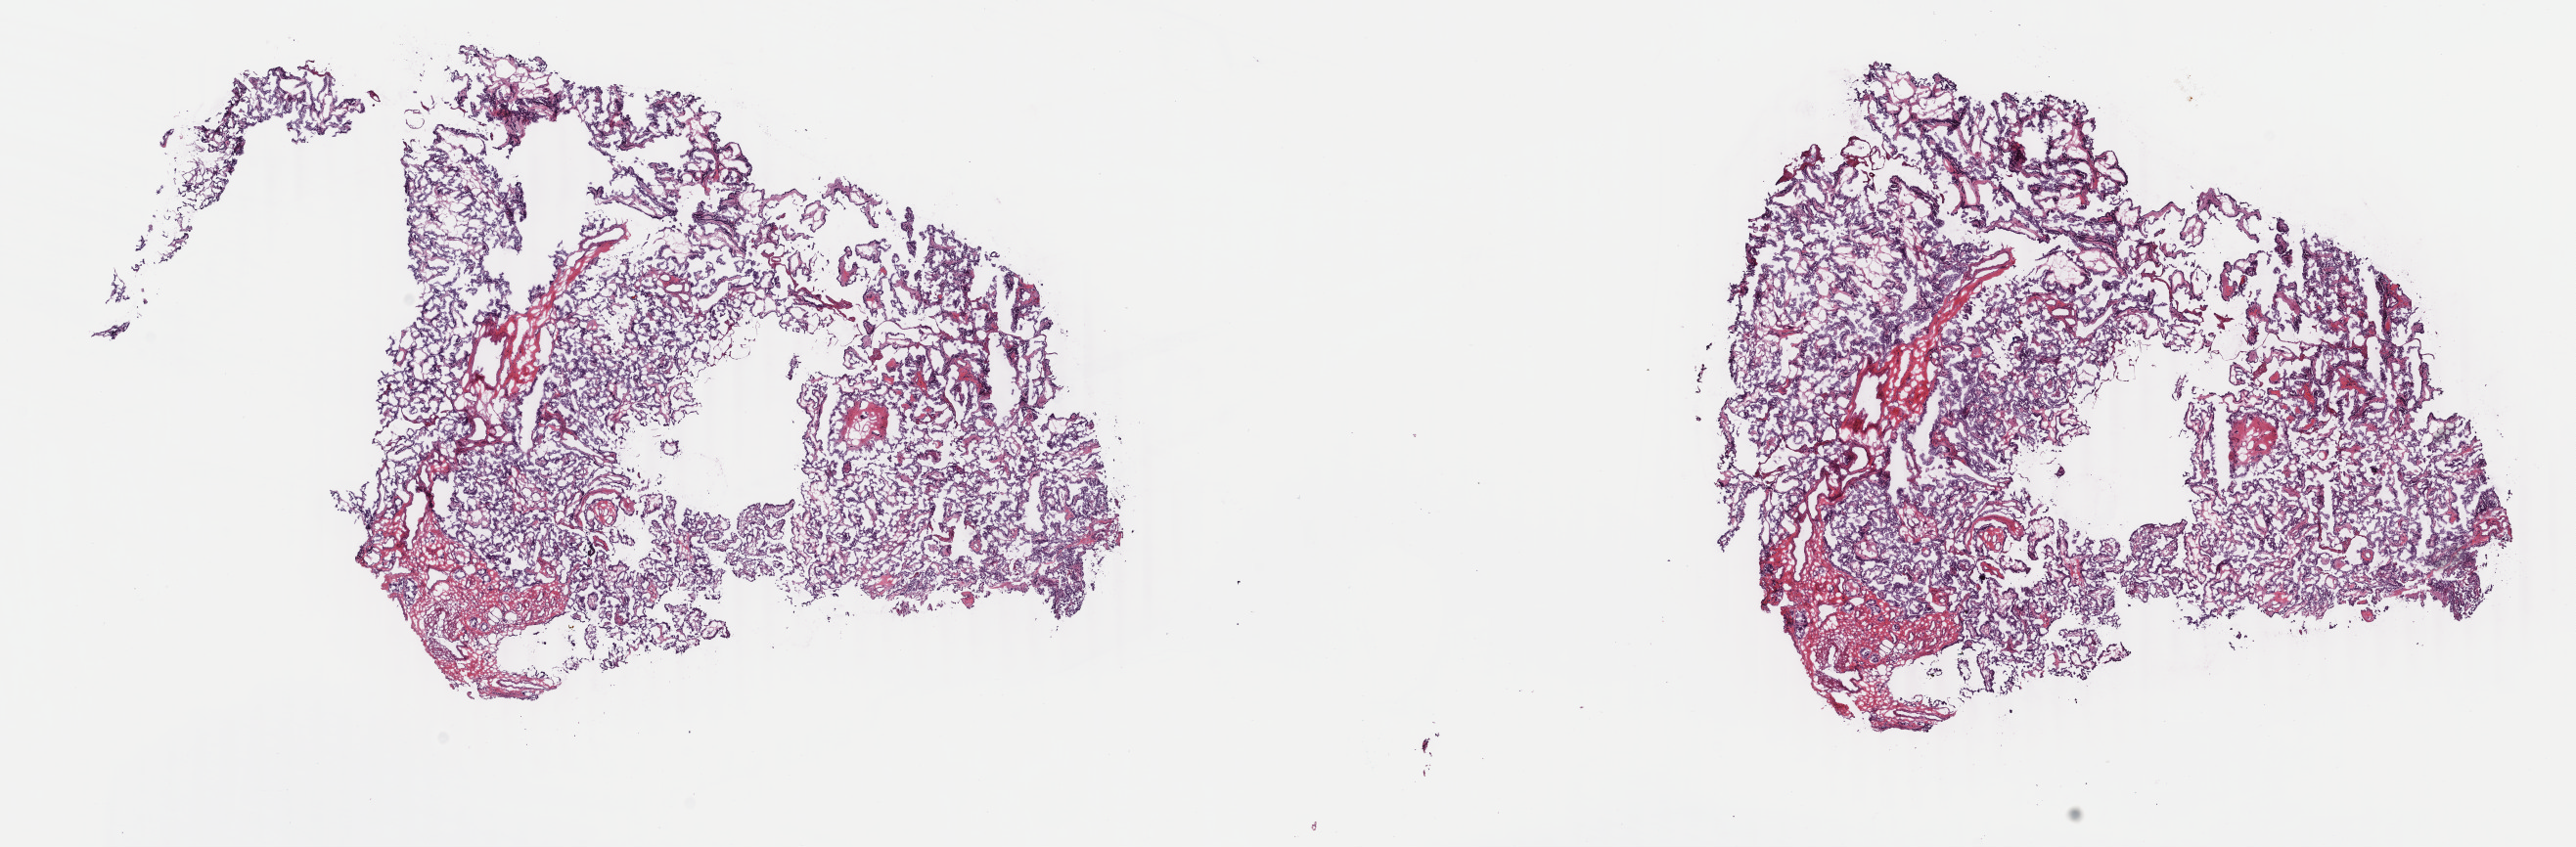
Digitized H&E-stained tissue section (whole slide), whole scanned area (about 20.9 x 6.9 mm) shown as a low-resolution overview, frozen section from the top of the tissue portion, primary tumour sample from the thyroid. Patient: female, age at initial diagnosis 49 years. Slide review estimates, as recorded: tumour cells 90%, tumour nuclei 85%, normal cells 0%, stromal cells 10%, necrosis 0%. Infiltration values recorded for this section: lymphocyte infiltration 2%, monocyte infiltration 0%, neutrophil infiltration 0%.
• AJCC pathologic stage: IVA (7th edition)
• histologic diagnosis: Papillary adenocarcinoma, NOS (thyroid gland)
• laterality: right